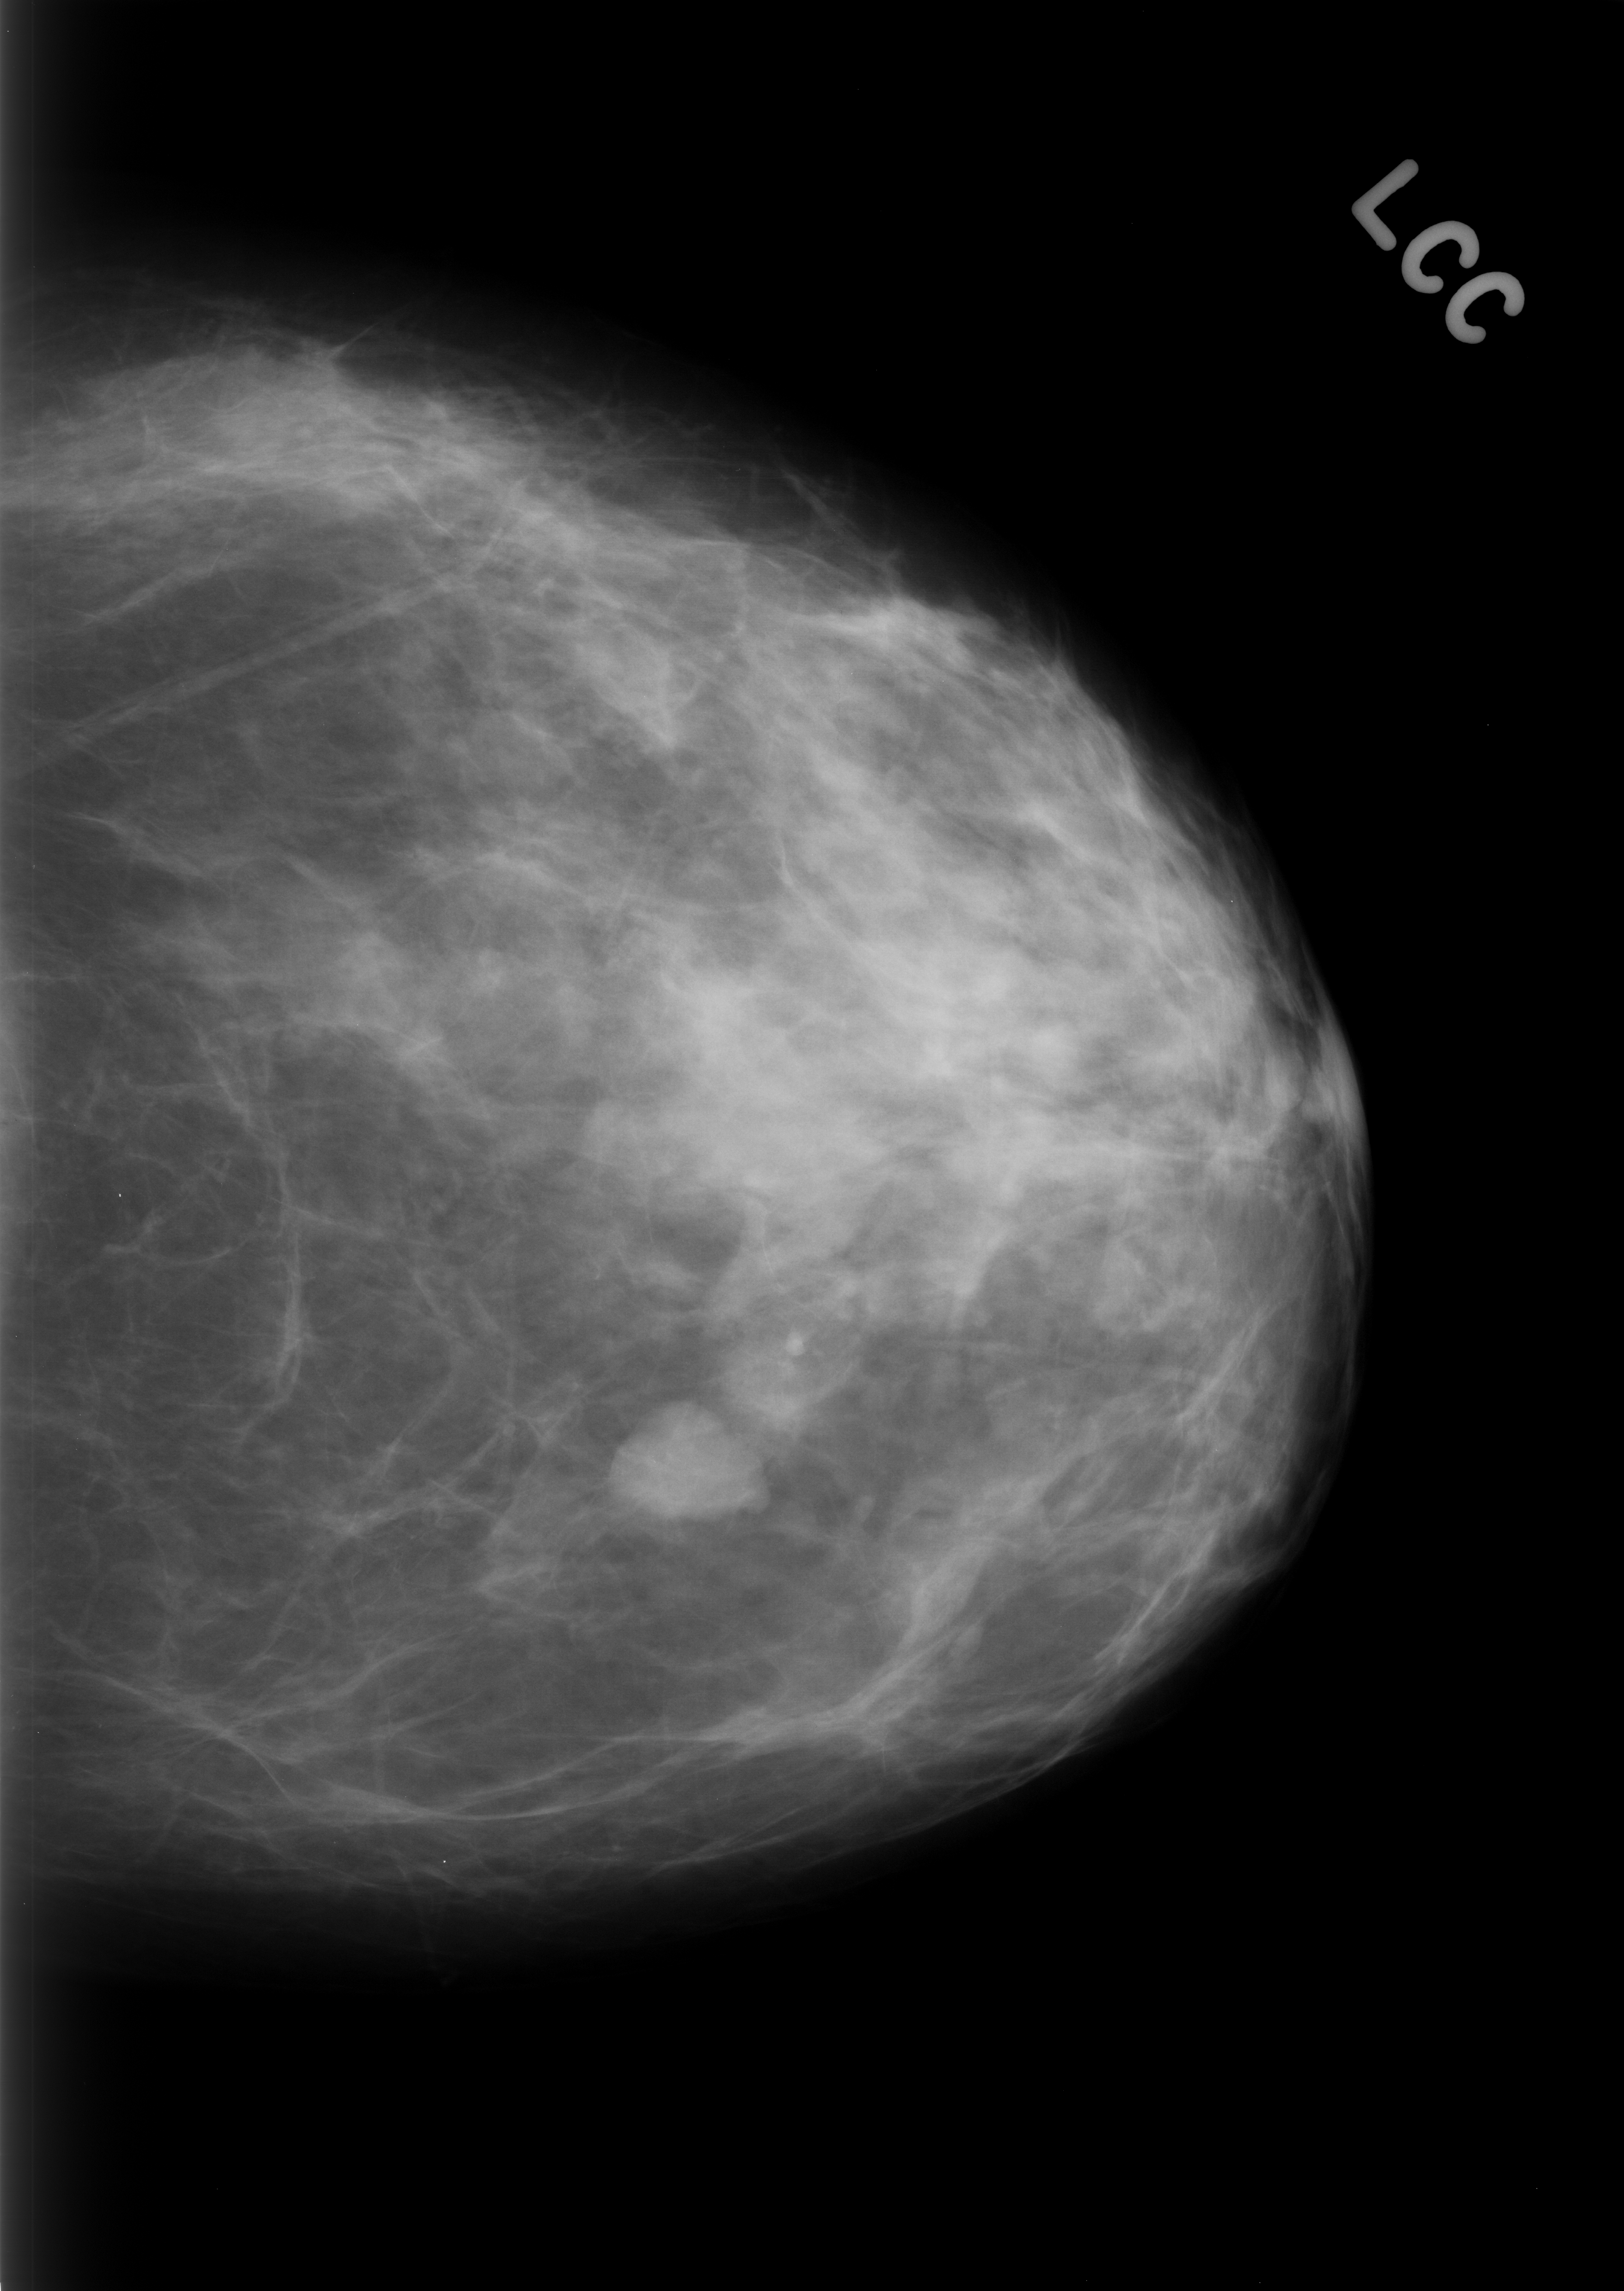
Mammogram (digitized film); left breast; craniocaudal (CC) view; breast composition: scattered fibroglandular densities (BI-RADS density category 2 of 4).
Marked findings (only marked abnormalities are described; nothing is implied about the rest of the image): mass, shape lobulated, margins circumscribed; BI-RADS assessment category 3; pathology (as recorded): benign.